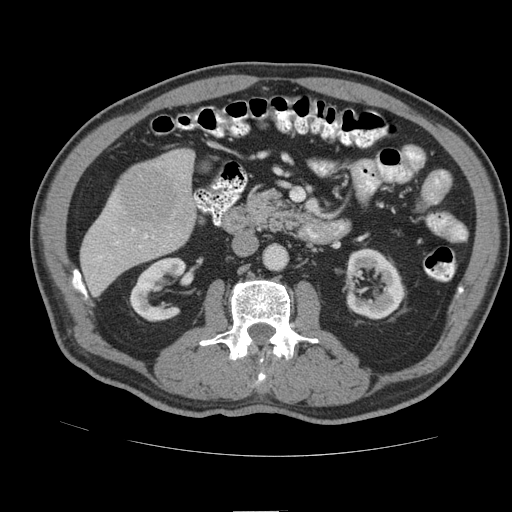
Contrast-enhanced abdominal CT (liver protocol), one axial slice; reconstruction kernel STANDARD; soft-tissue window (W 400 / L 40 HU); 512 × 512 image matrix, field of view 380 × 380 mm. From the clinical record (not read from this slice): diagnosis: hepatocellular carcinoma (patient treated with transarterial chemoembolisation; whether this scan precedes or follows treatment is not stated here); TNM stage (as recorded): Stage-IIIB; Child-Pugh class: A.
Structures marked on this image (semi-automatic segmentation, software-assisted and operator-edited):
- liver parenchyma outside the tumour (the mass and vessels are separate outlines, so this box may not span the whole liver): bounding box <80,150,196,294> (left, top, right, bottom; pixels)
- mass: <122,165,177,227>
- liver vessels: <99,256,101,258>